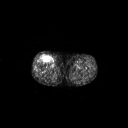
FDG PET of an extremity soft-tissue mass (from a PET/CT study), one axial slice; slice 266 of 311 in the series (ordered by position); 3.27 mm slice thickness; 128 × 128 image matrix, field of view 700 × 700 mm. Male patient, age 56 years. Case-level facts recorded for this patient, not image findings: histological type: pleiomorphic leiomyosarcoma; grade: intermediate; site of the primary tumour: right thigh.
Structures marked on this image (expert contour drawn on MRI and transferred to this co-registered scan by the dataset authors):
- gross tumour volume including surrounding oedema: bounding box <40,55,51,62> (left, top, right, bottom; pixels)
- gross tumour volume (mass): <42,56,50,62>